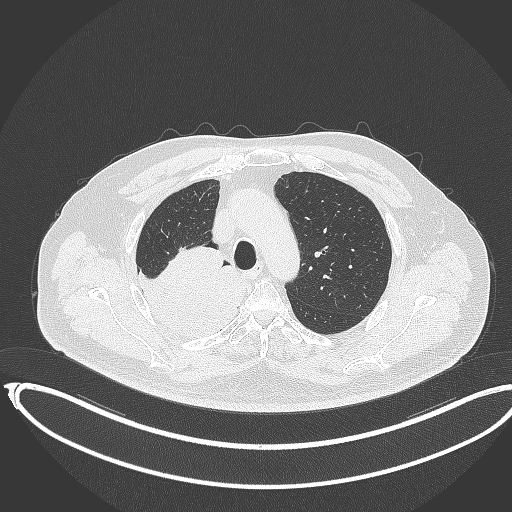
Chest CT, one axial slice; slice 275 of 403 in the series (ordered by position); lung window (W 1500 / L -600 HU); 1 mm slice thickness; 512 × 512 image matrix, field of view 436 × 436 mm. Patient: male, 68 years. From the clinical record (not read from this slice): clinical TNM (as recorded): T2a N0 M0.
Annotated regions visible in this slice (bounding box drawn by a radiologist):
- lung tumour (recorded histology: adenocarcinoma): bounding box (x1, y1, x2, y2) in pixels: (128, 236, 255, 353)